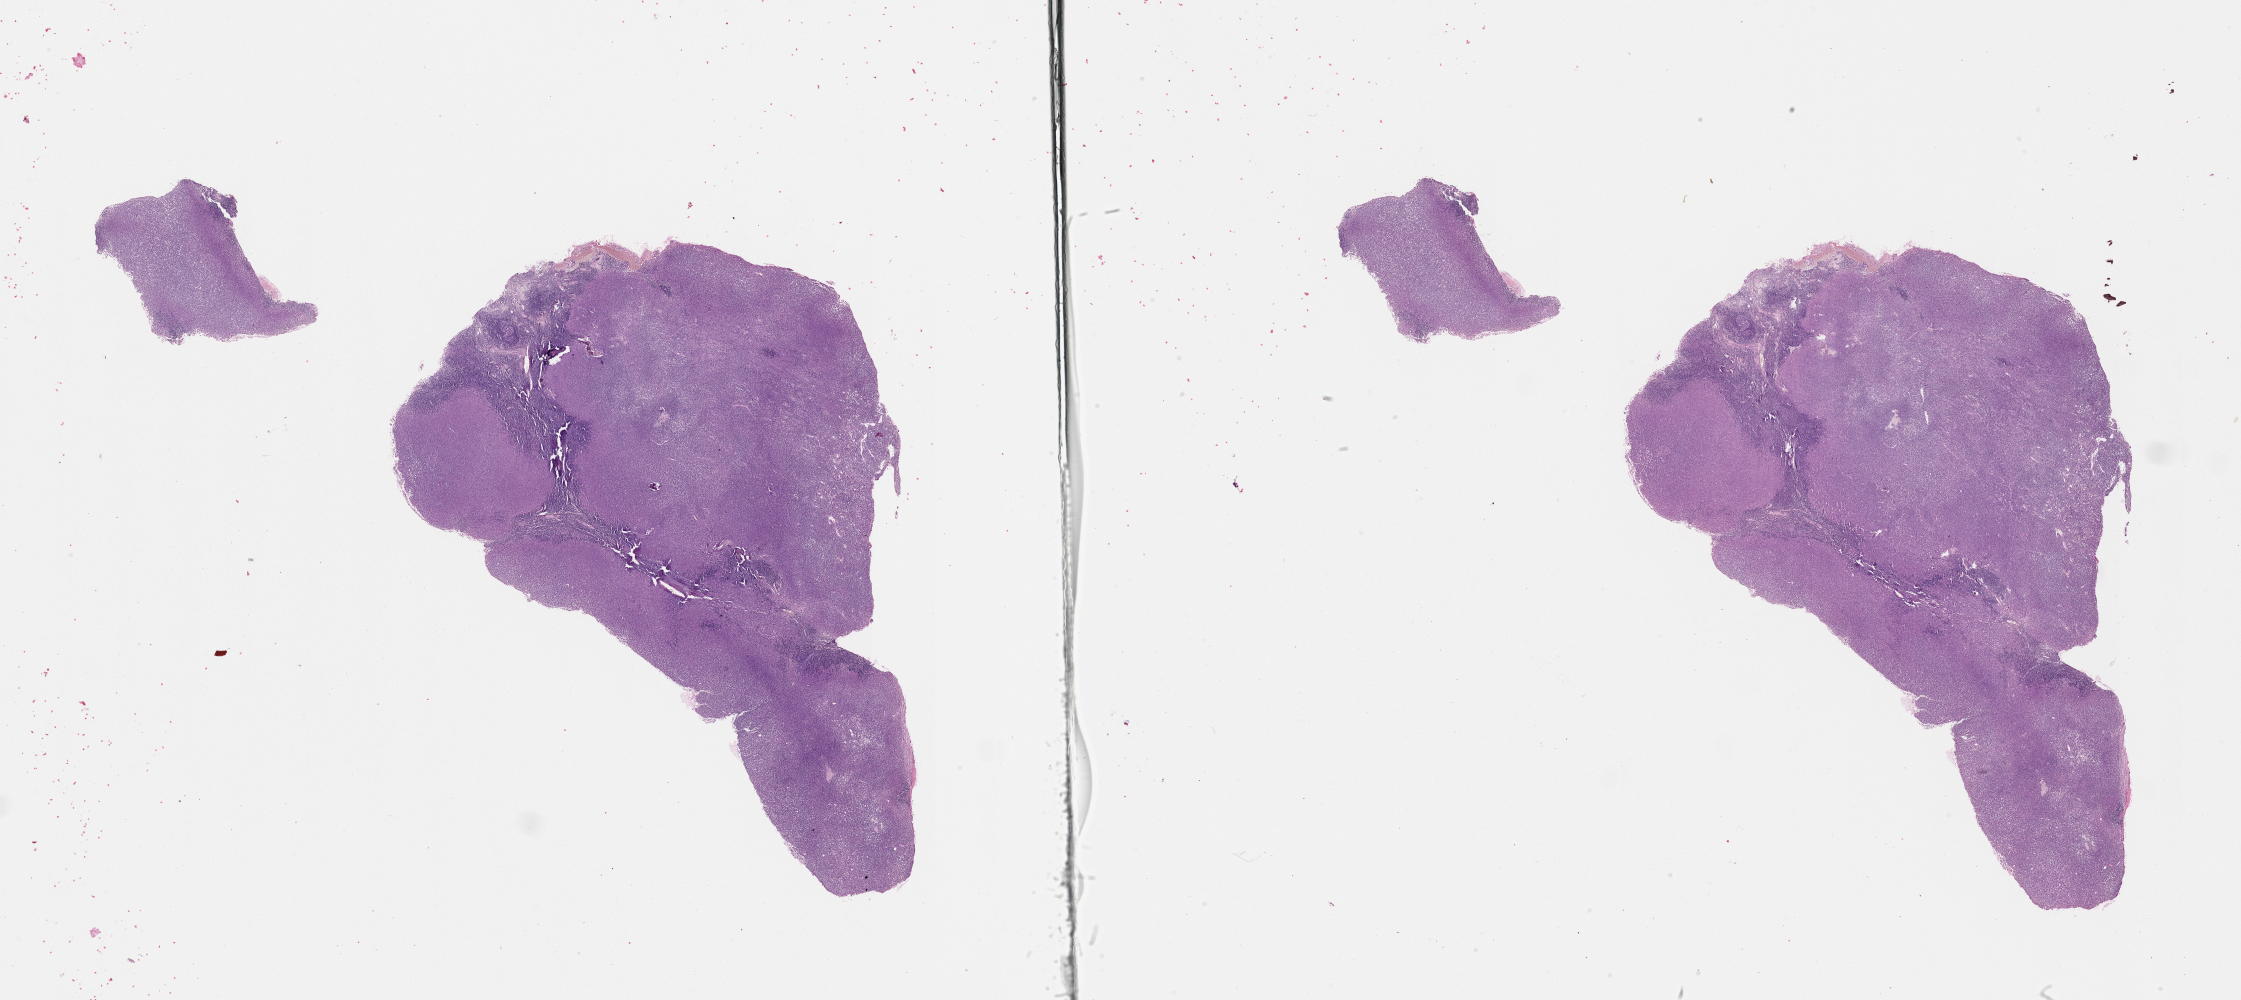
Whole-slide histology image, H&E — whole scanned area (about 36.1 x 16.1 mm) shown as a low-resolution overview. Patient: female, age 80 years.
• patient diagnosis: Malignant melanoma, NOS